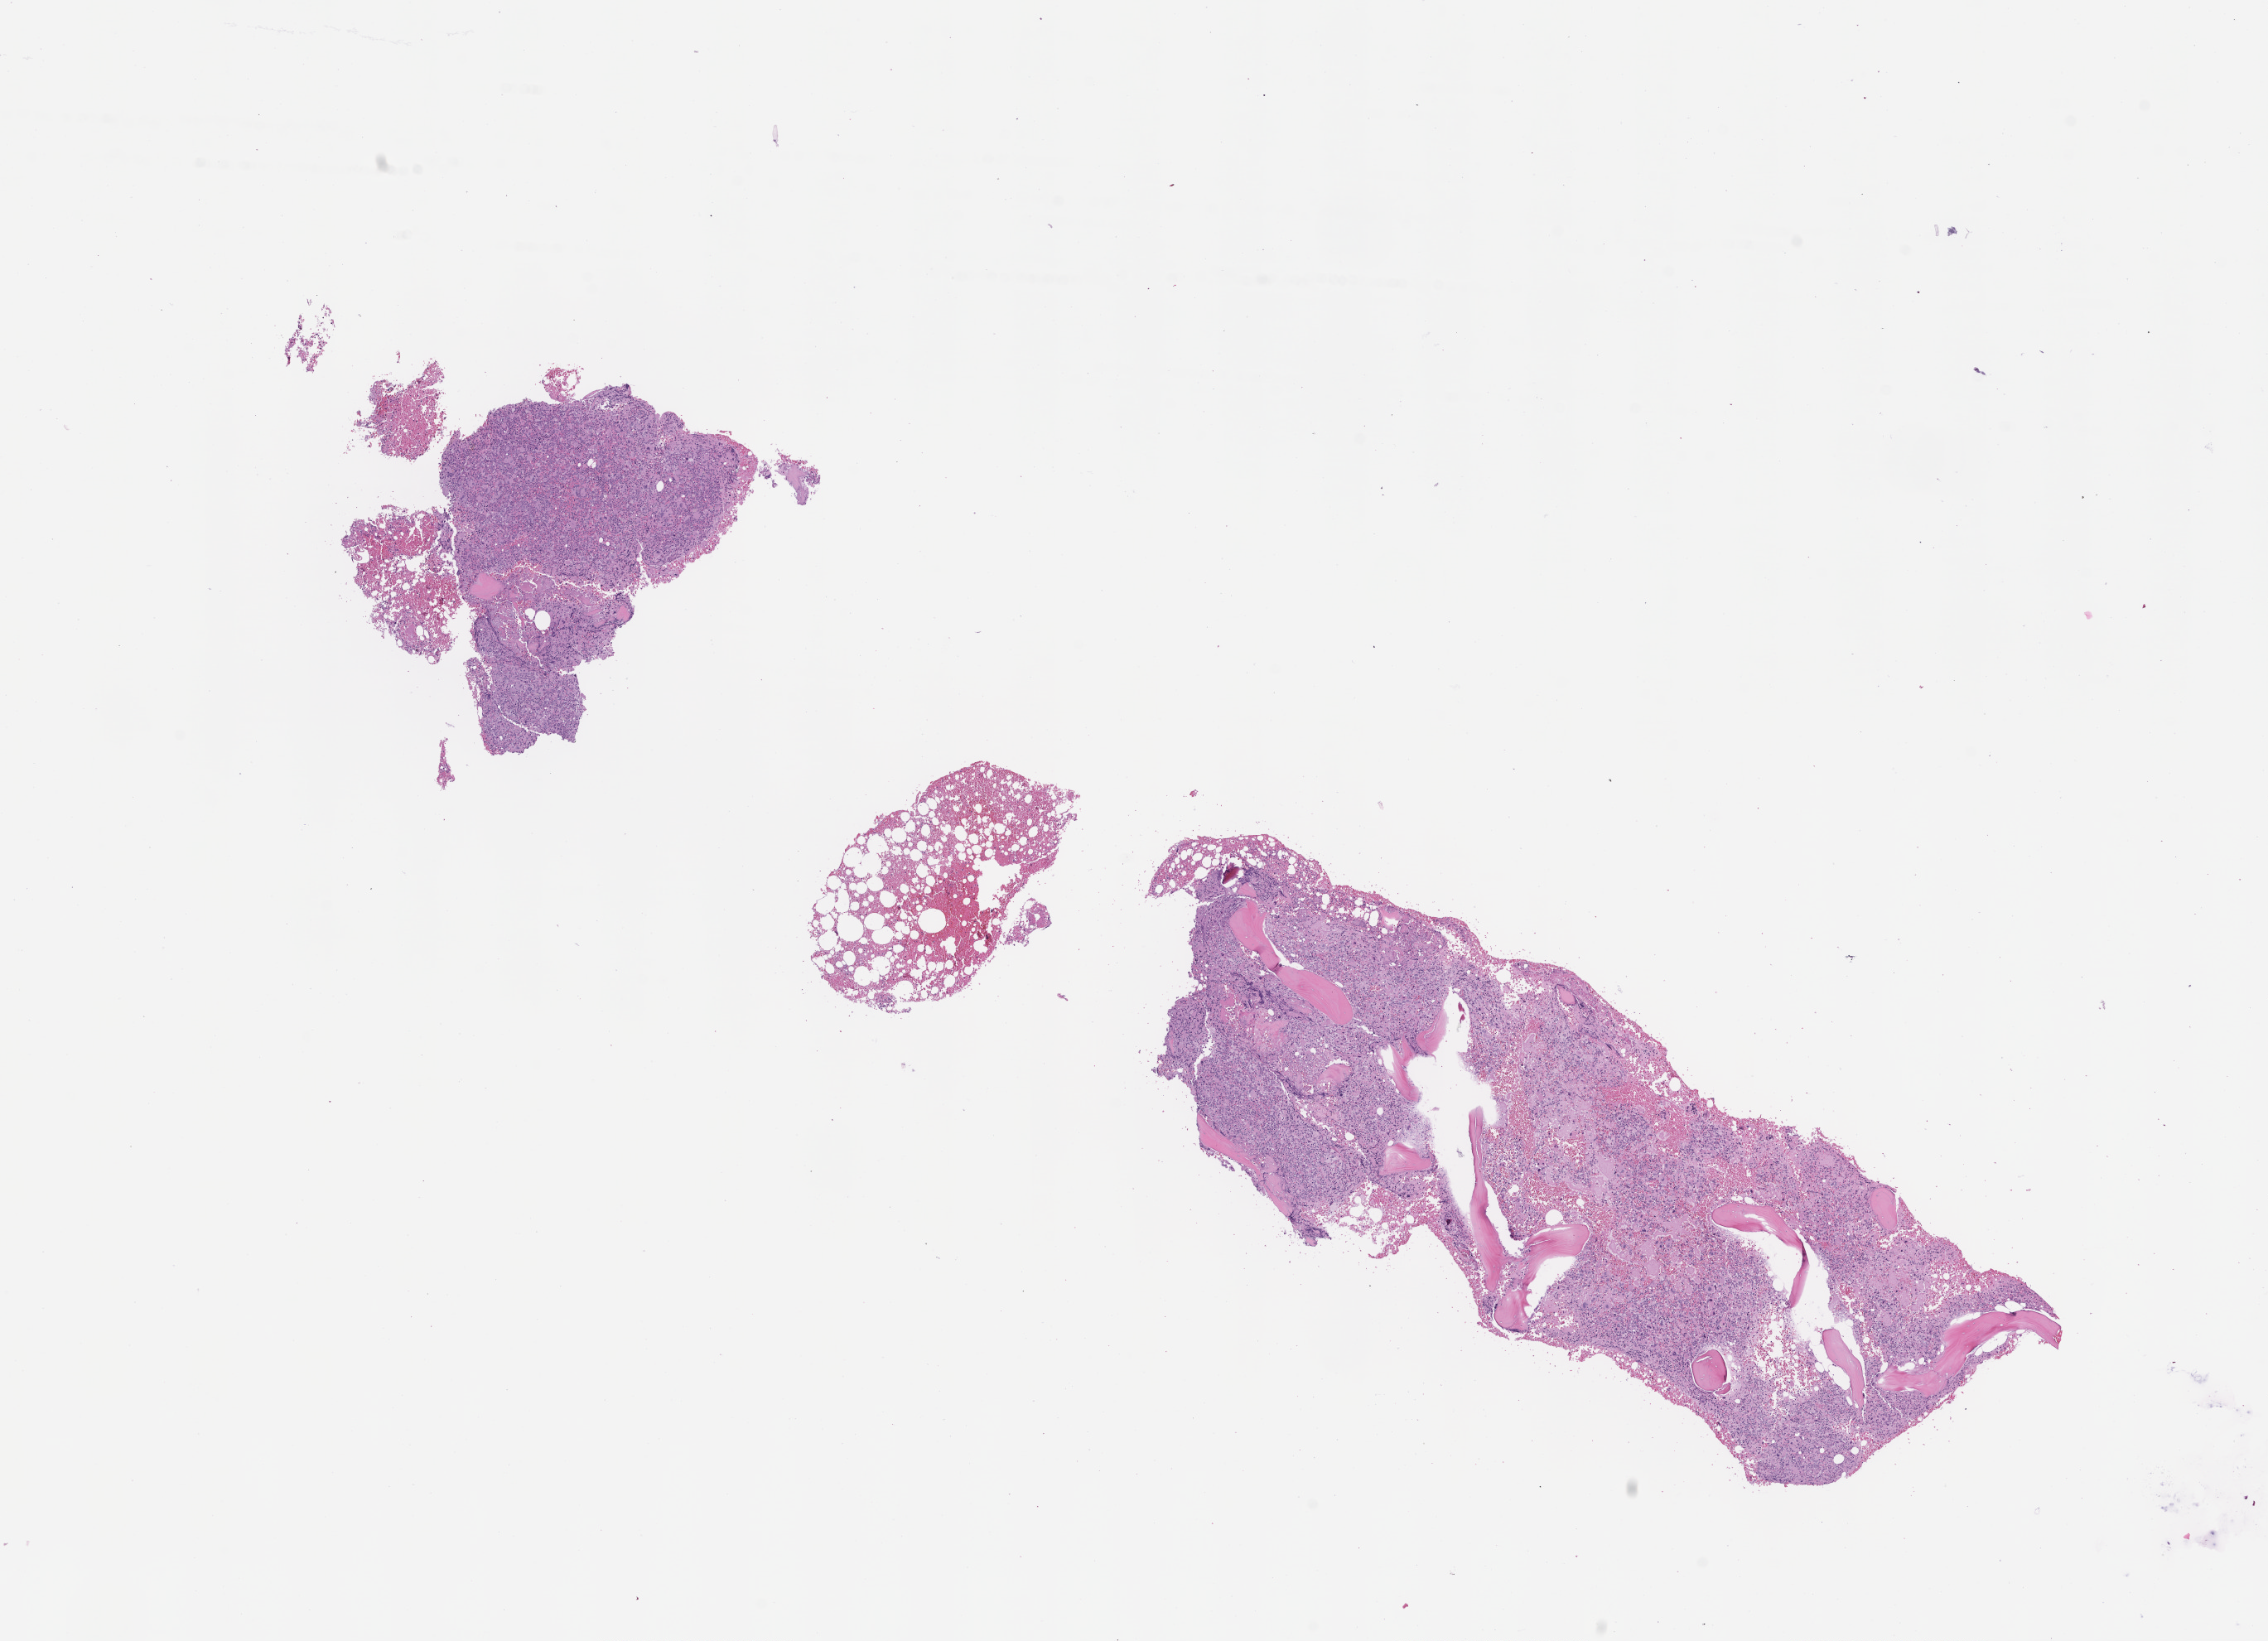
Whole-slide image, haematoxylin and eosin stain — whole scanned area (about 11.1 x 8.0 mm) shown as a low-resolution overview. Formalin-fixed, paraffin-embedded (FFPE) tissue. Tissue site: bone marrow. Archival tissue. Patient sex: male.
This section: primary tumour tissue. Diagnosis: Acute Myeloid Leukemia Not Otherwise Specified.